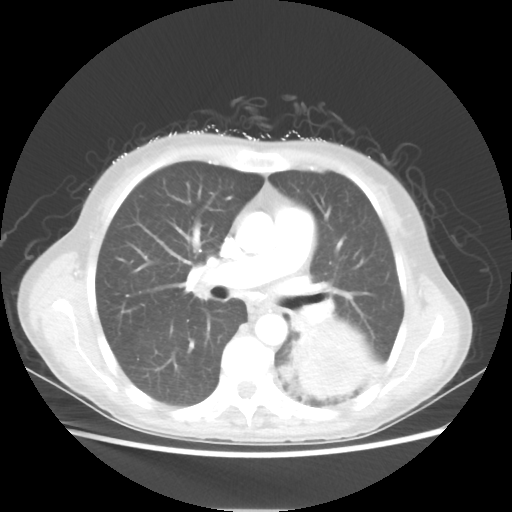
Chest CT, one axial slice. Slice 32 of 56 in the series (ordered by position). Lung window (W 1500 / L -600 HU). 5 mm slice thickness. 512 × 512 image matrix. Female patient, age 53 years. Case-level facts recorded for this patient, not image findings: clinical TNM (as recorded): T3 N0 M0.
Annotated regions visible in this slice (rectangle marked by the reading radiologist):
- lung tumour (recorded histology: adenocarcinoma): bounding box <291,318,372,397> (left, top, right, bottom; pixels)